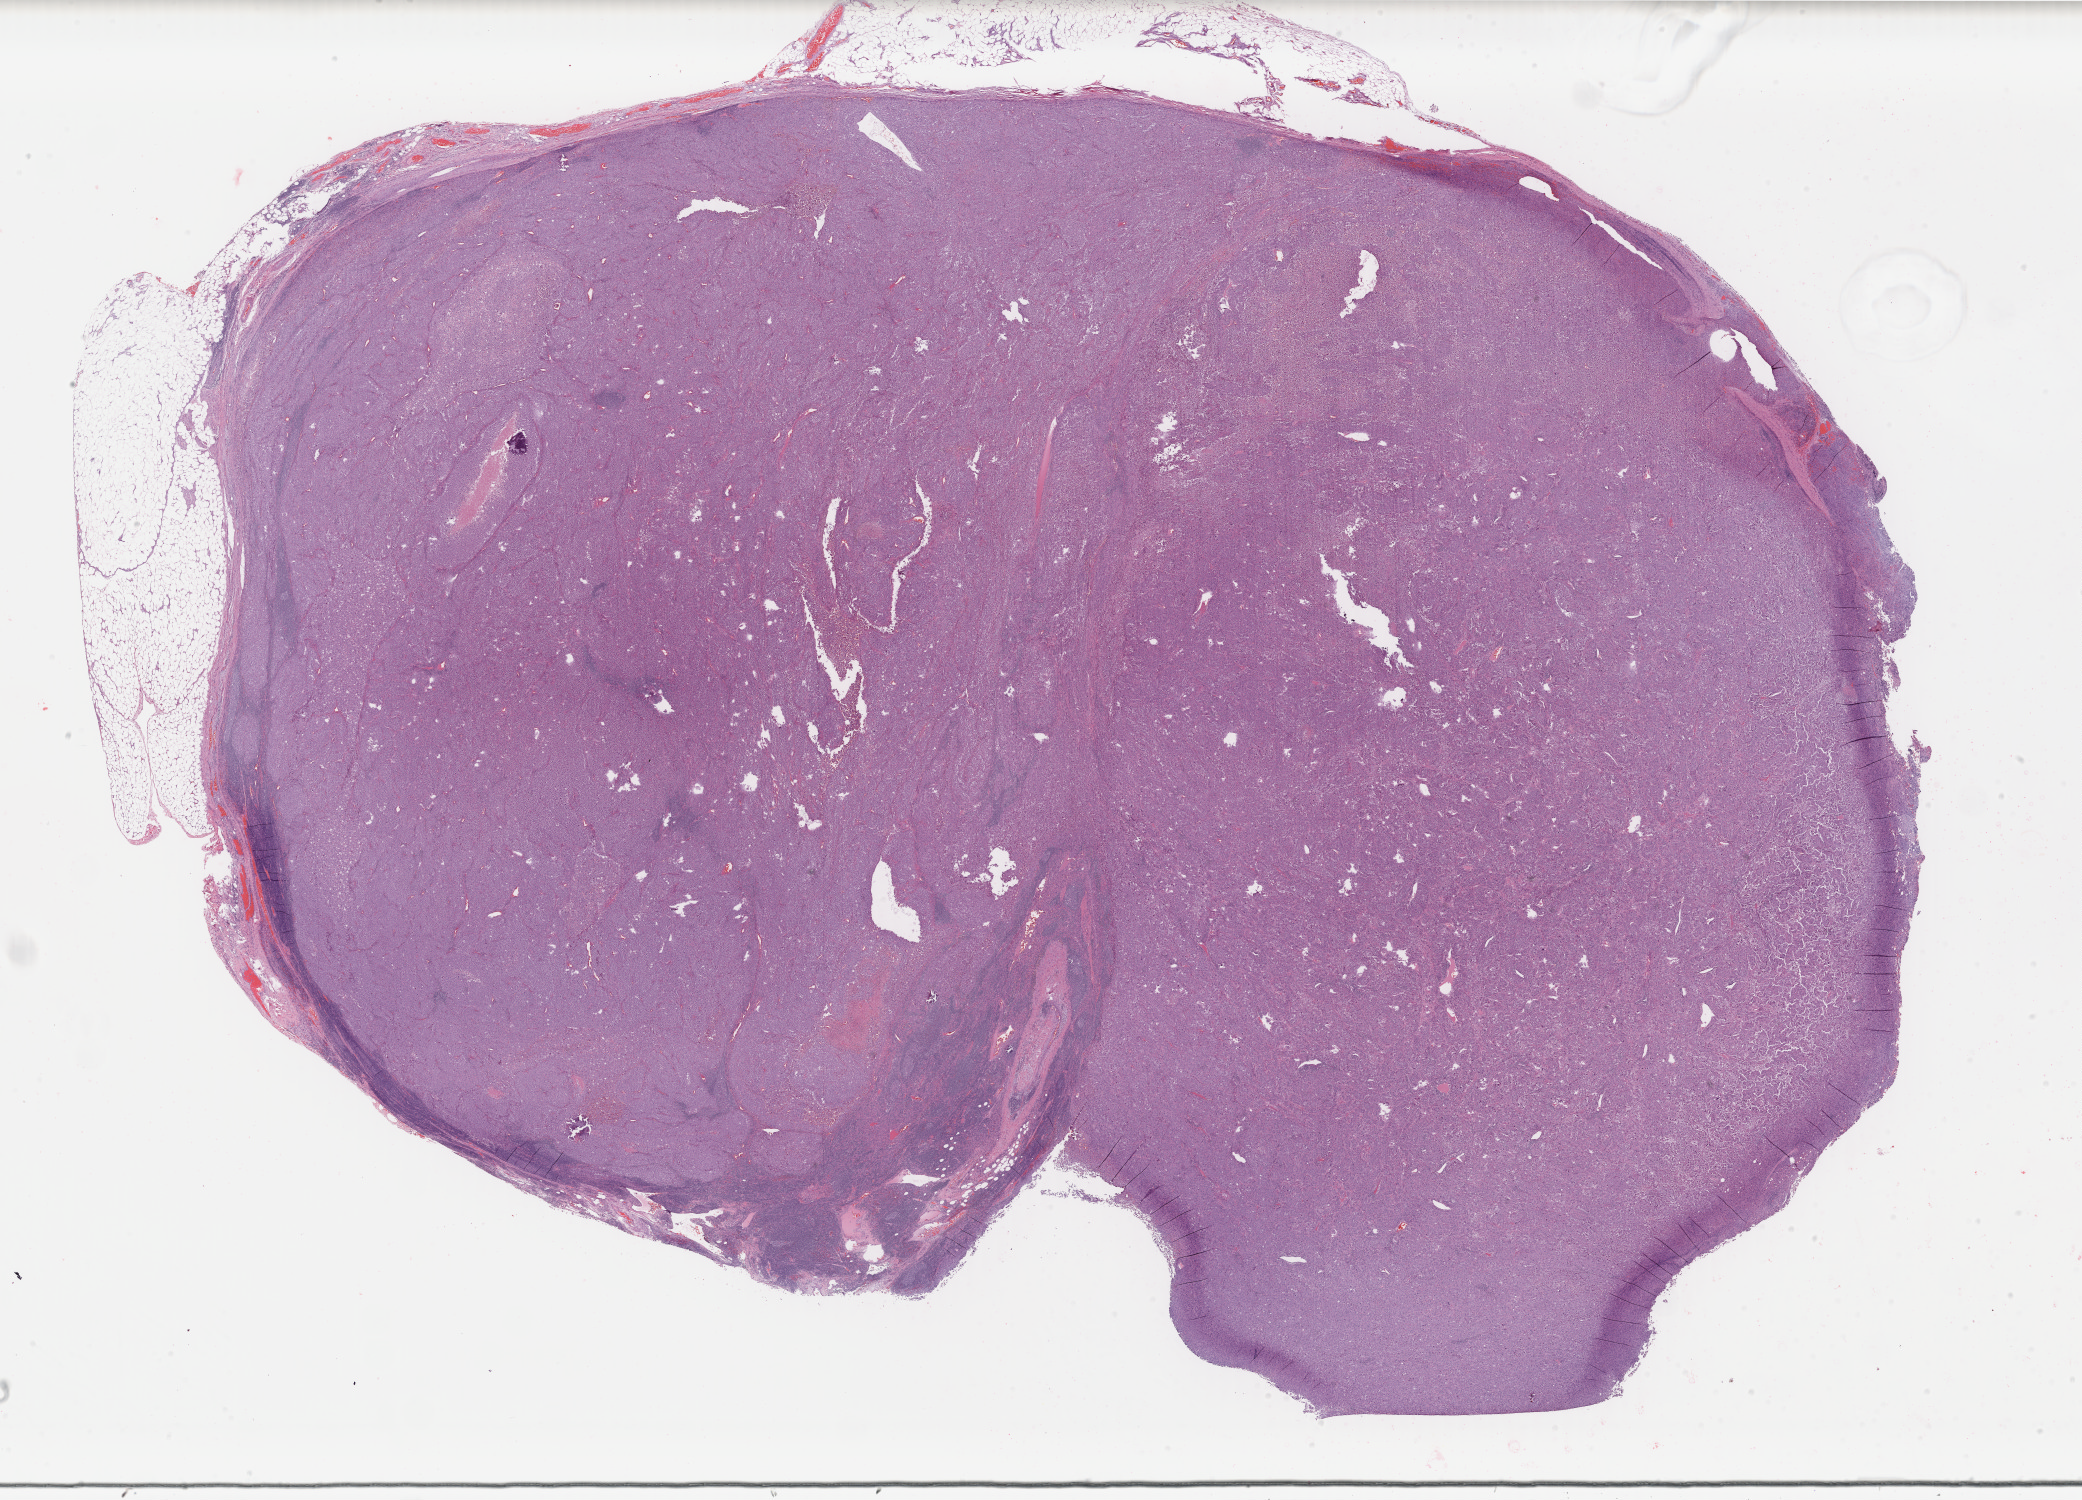
Whole-slide histology image, H&E — shown as a low-resolution overview of the whole scanned area (about 33.1 x 23.8 mm, acquisition: 40x scan), formalin-fixed paraffin-embedded (FFPE) diagnostic section, skin, primary tumour sample. Male patient; age at initial diagnosis 38 years.
* diagnosis: Malignant melanoma, NOS